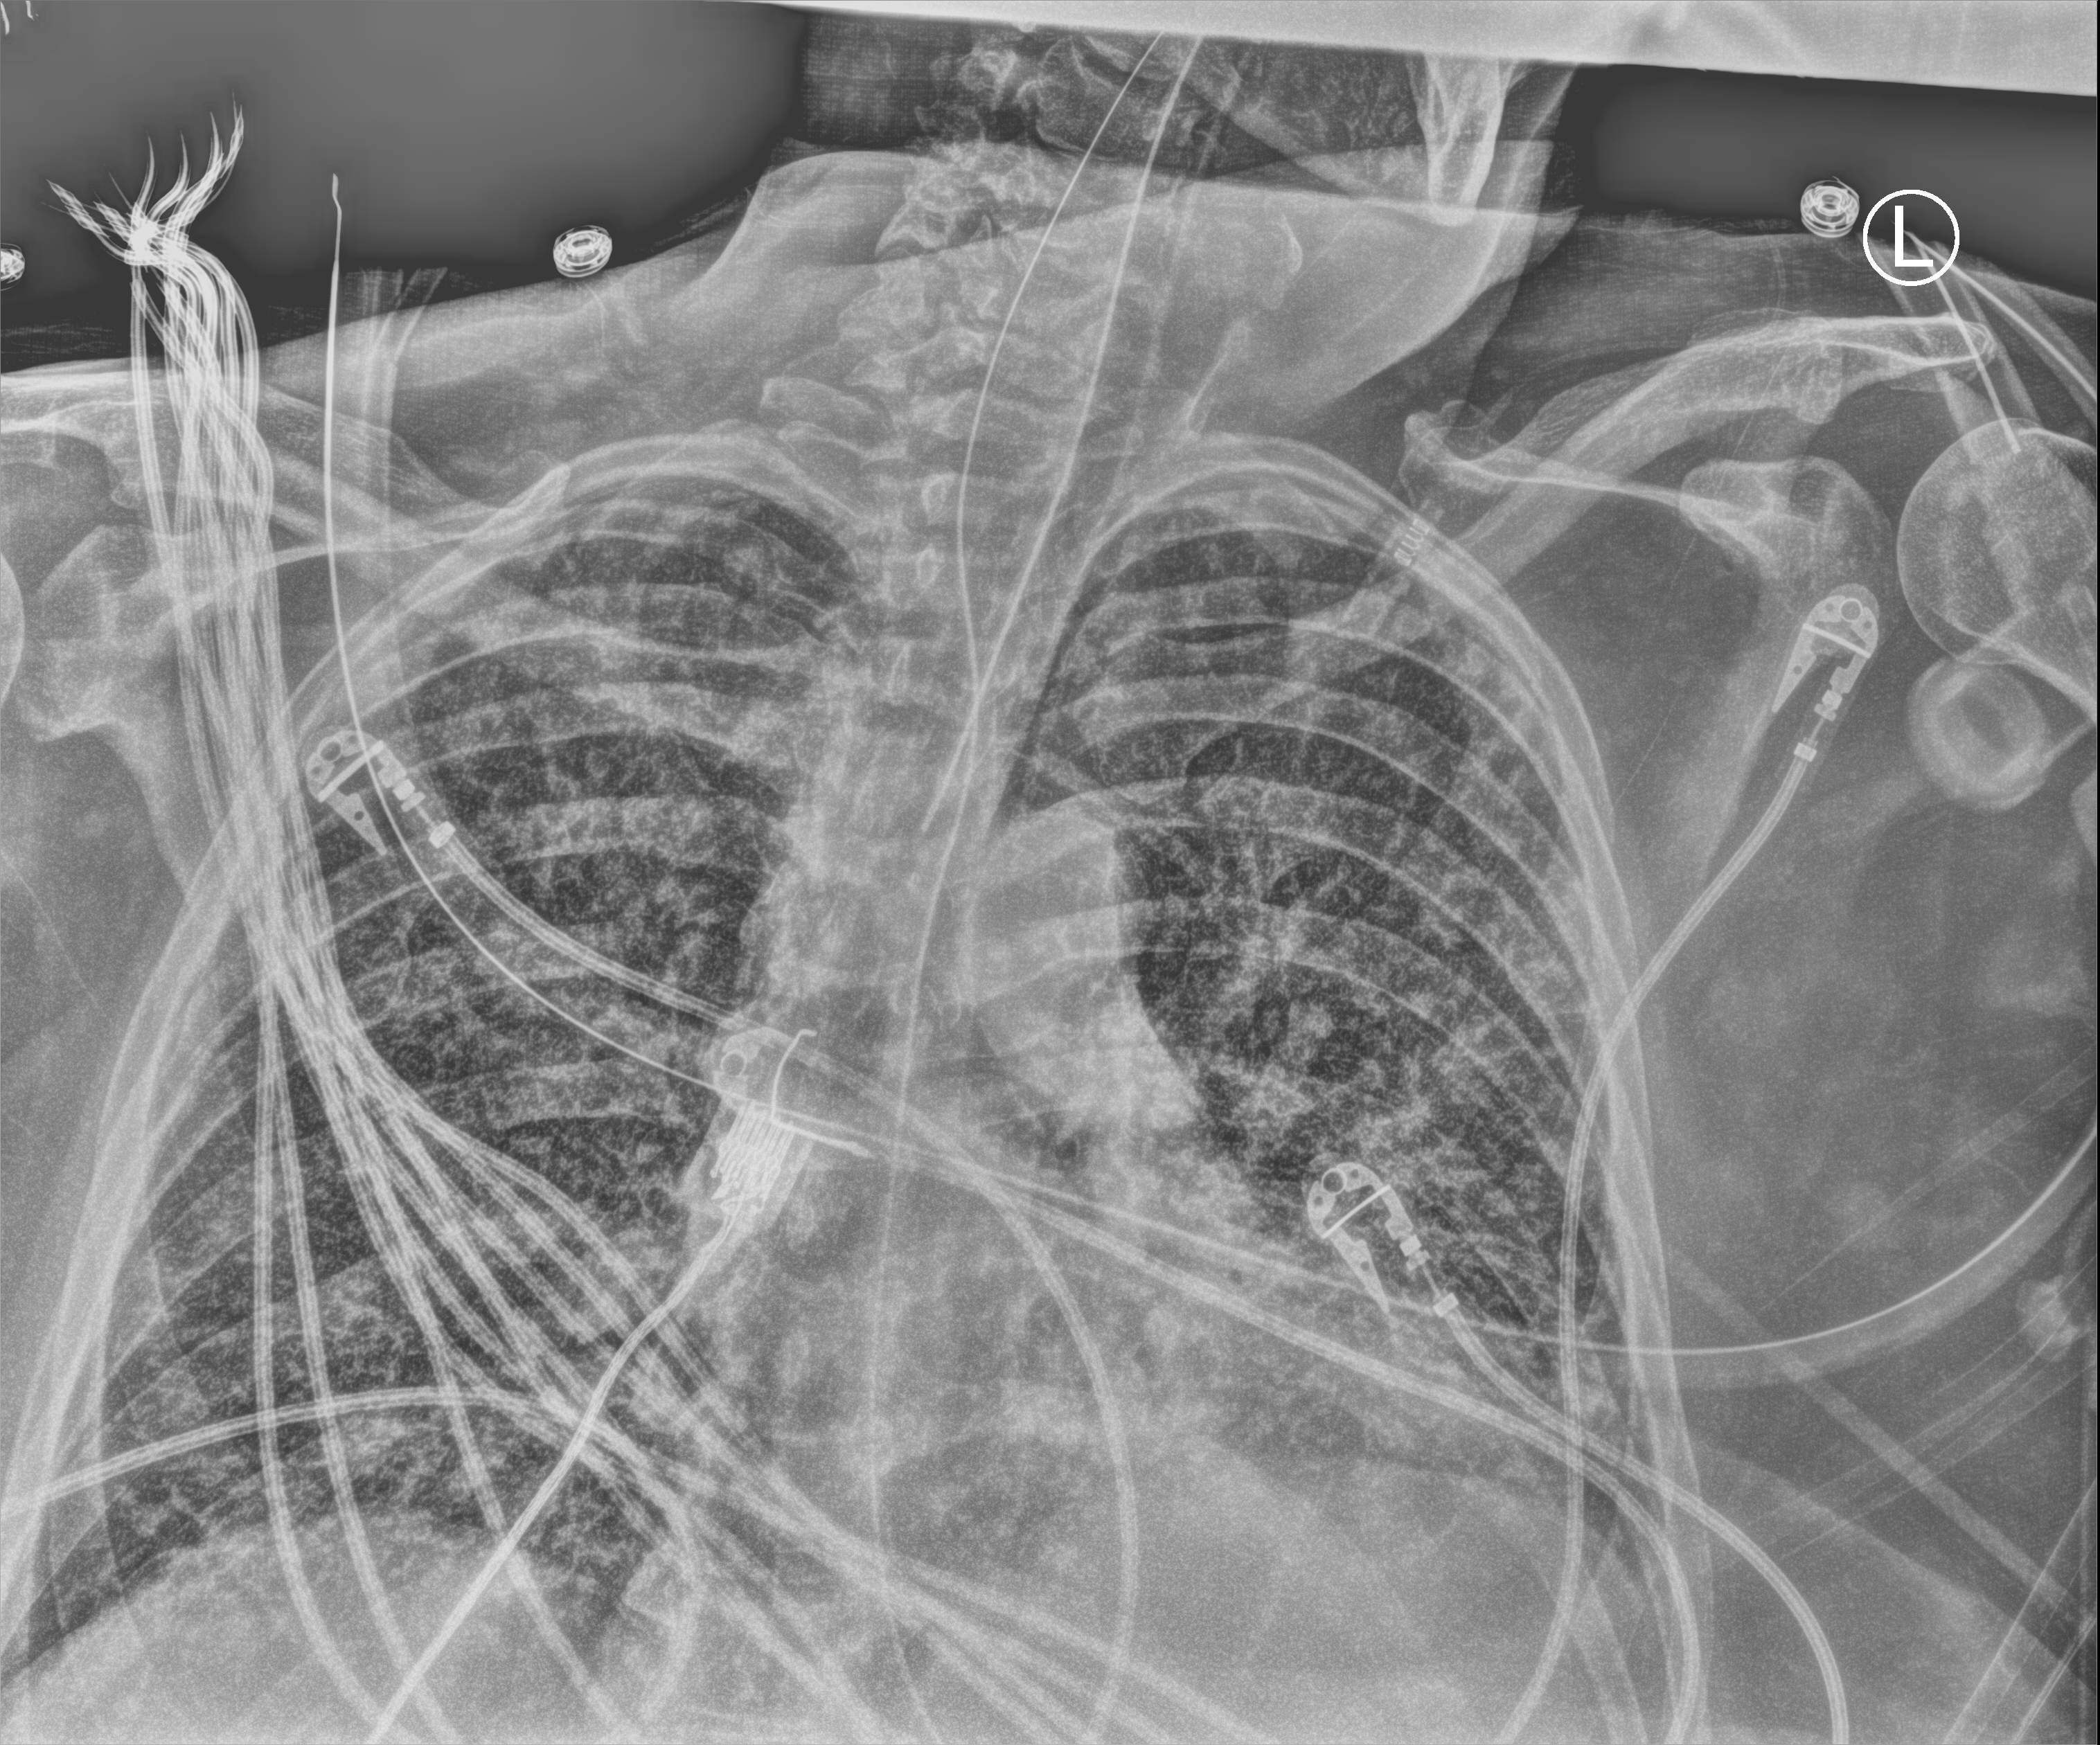
Chest X-ray (portable); anteroposterior (AP) projection. Patient hospitalised with COVID-19, aged 18–59 years.
Admission-level facts for this patient (not findings on this image; timing relative to this image not recorded):
- length of hospital stay: 28 days